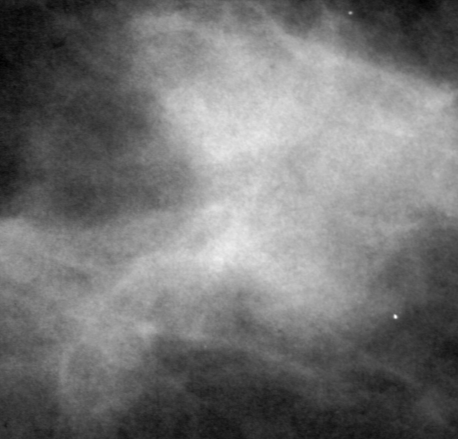
Region of interest cut from a scanned film mammogram (one marked finding), right breast, CC view.
Marked abnormality: mass, shape irregular, margins ill defined; BI-RADS assessment category 3; subtlety rating 5 on a 1 (subtle) to 5 (obvious) scale; pathology (as recorded): malignant.